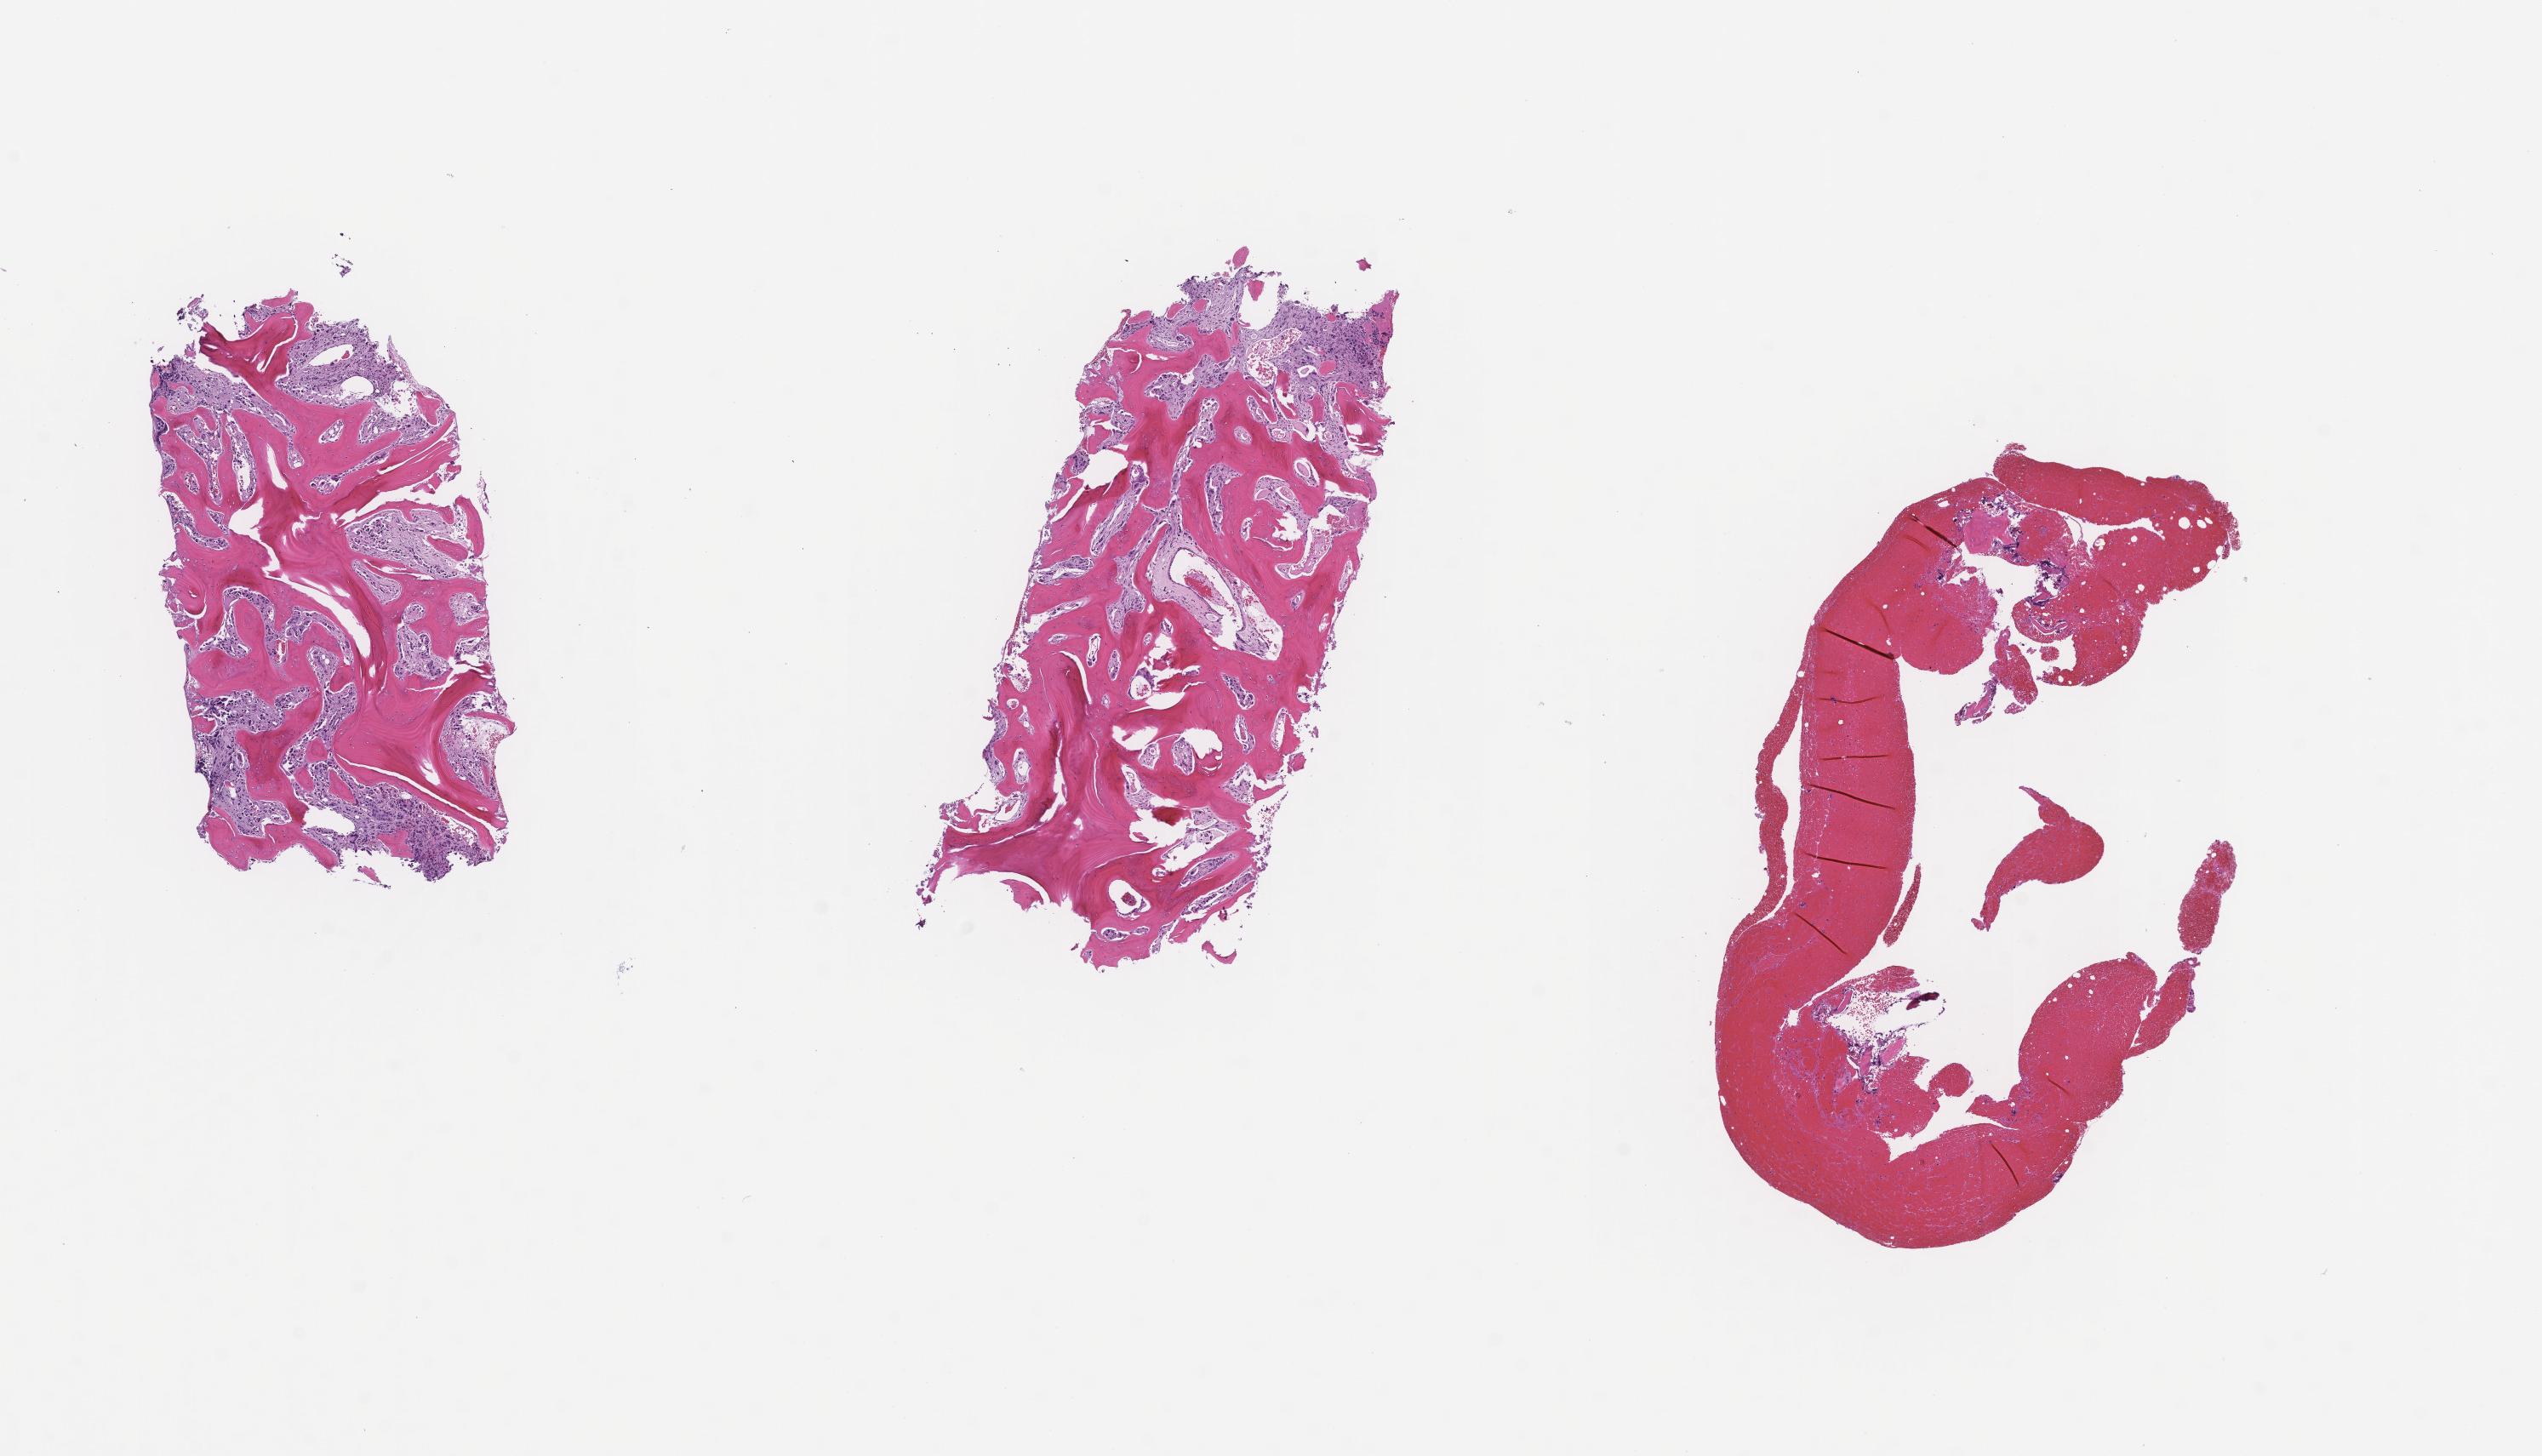
Hematoxylin and eosin (H&E) whole-slide image, shown as a low-resolution overview of the whole scanned area (about 12.1 x 6.9 mm); formalin-fixed paraffin-embedded section. Patient sex: female.
This section: metastasis (sampled organ not recorded). Patient diagnosis (primary): Invasive Breast Carcinoma.